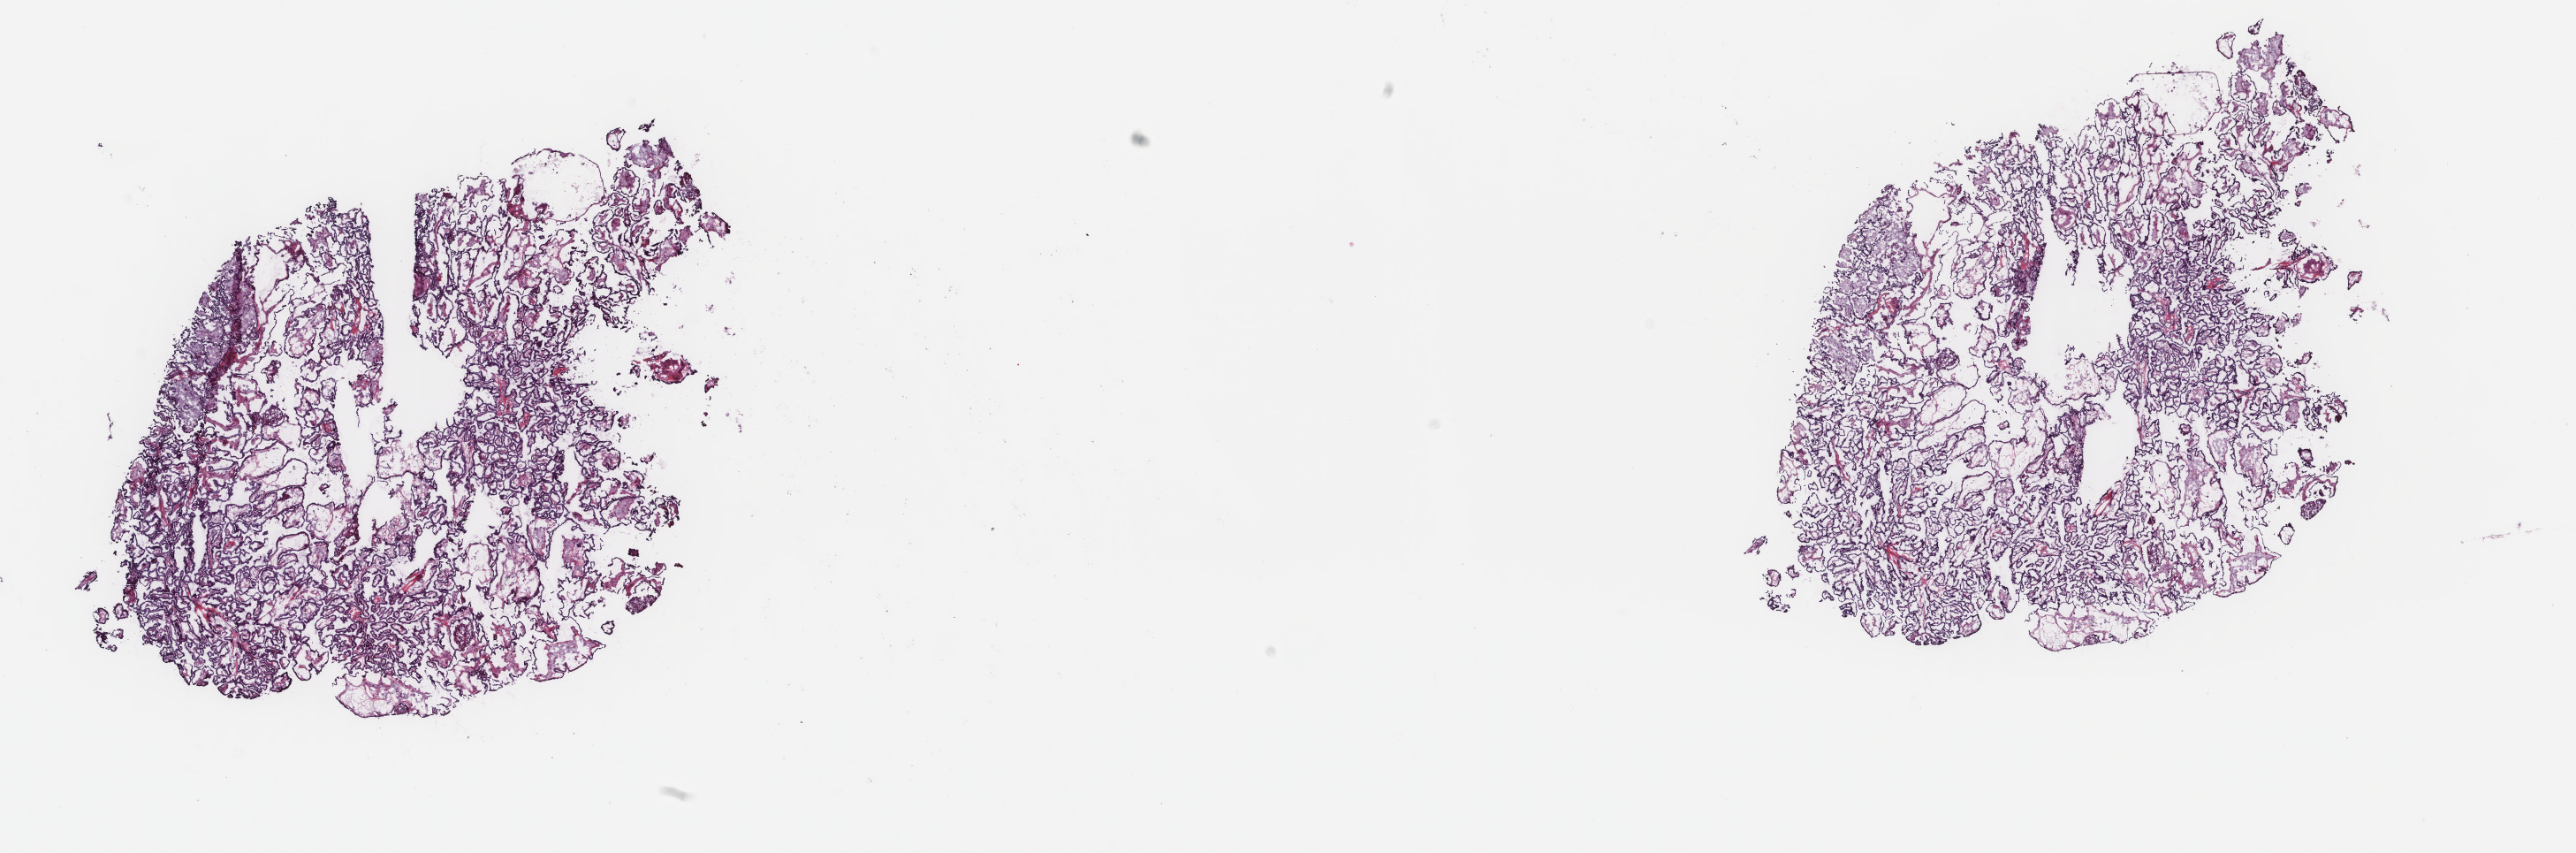
H&E whole-slide image, low-resolution overview of the scanned area, about 23.1 x 7.7 mm (from a 40x scan). Frozen section from the top of the tissue portion. Primary tumour sample from the thyroid. Female patient; age at initial diagnosis 47 years. Slide review estimates, as recorded: tumour cells 100%, tumour nuclei 88%, normal cells 0%, stromal cells 0%, necrosis 0%. Inflammatory infiltration, as recorded: lymphocyte infiltration 0%, monocyte infiltration 0%, neutrophil infiltration 0%.
AJCC pathologic stage: II (6th edition). Pathologic diagnosis: Papillary adenocarcinoma, NOS (thyroid gland). Laterality: right.